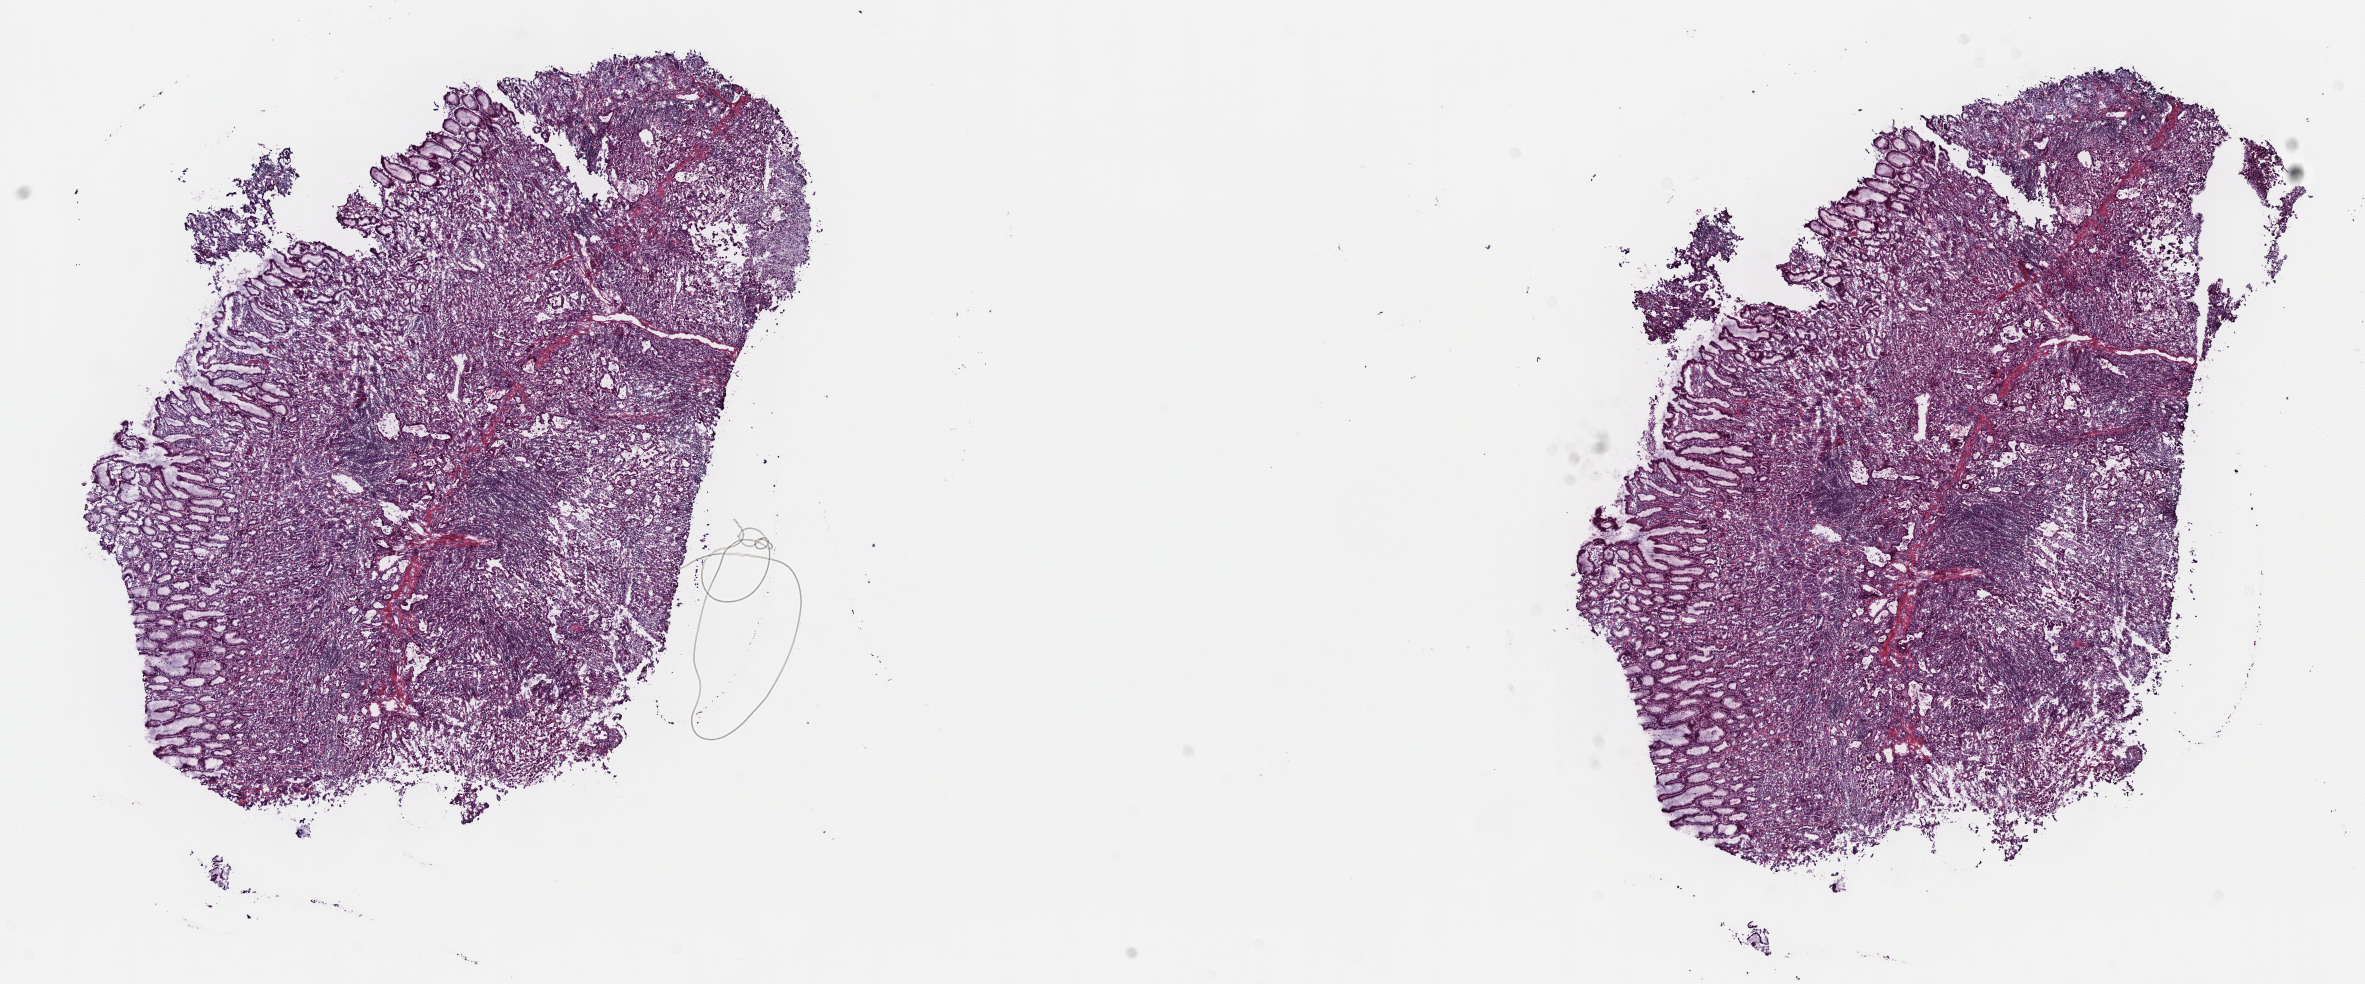
Hematoxylin and eosin (H&E) stained whole-slide image, low-resolution overview of the scanned area, about 19.1 x 8.0 mm, frozen section from the top of the tissue portion, primary tumour sample from the stomach. Male patient; age at initial diagnosis 57 years. Histologic grade: G2 (moderately differentiated). Slide review estimates, as recorded: tumour cells 60%, tumour nuclei 60%, normal cells 20%, stromal cells 20%, necrosis 0%. Infiltration values recorded for this section: lymphocyte infiltration 40%, monocyte infiltration 20%, neutrophil infiltration 20%.
* diagnosis: Adenocarcinoma, NOS
* AJCC pathologic stage: IIB (7th edition)